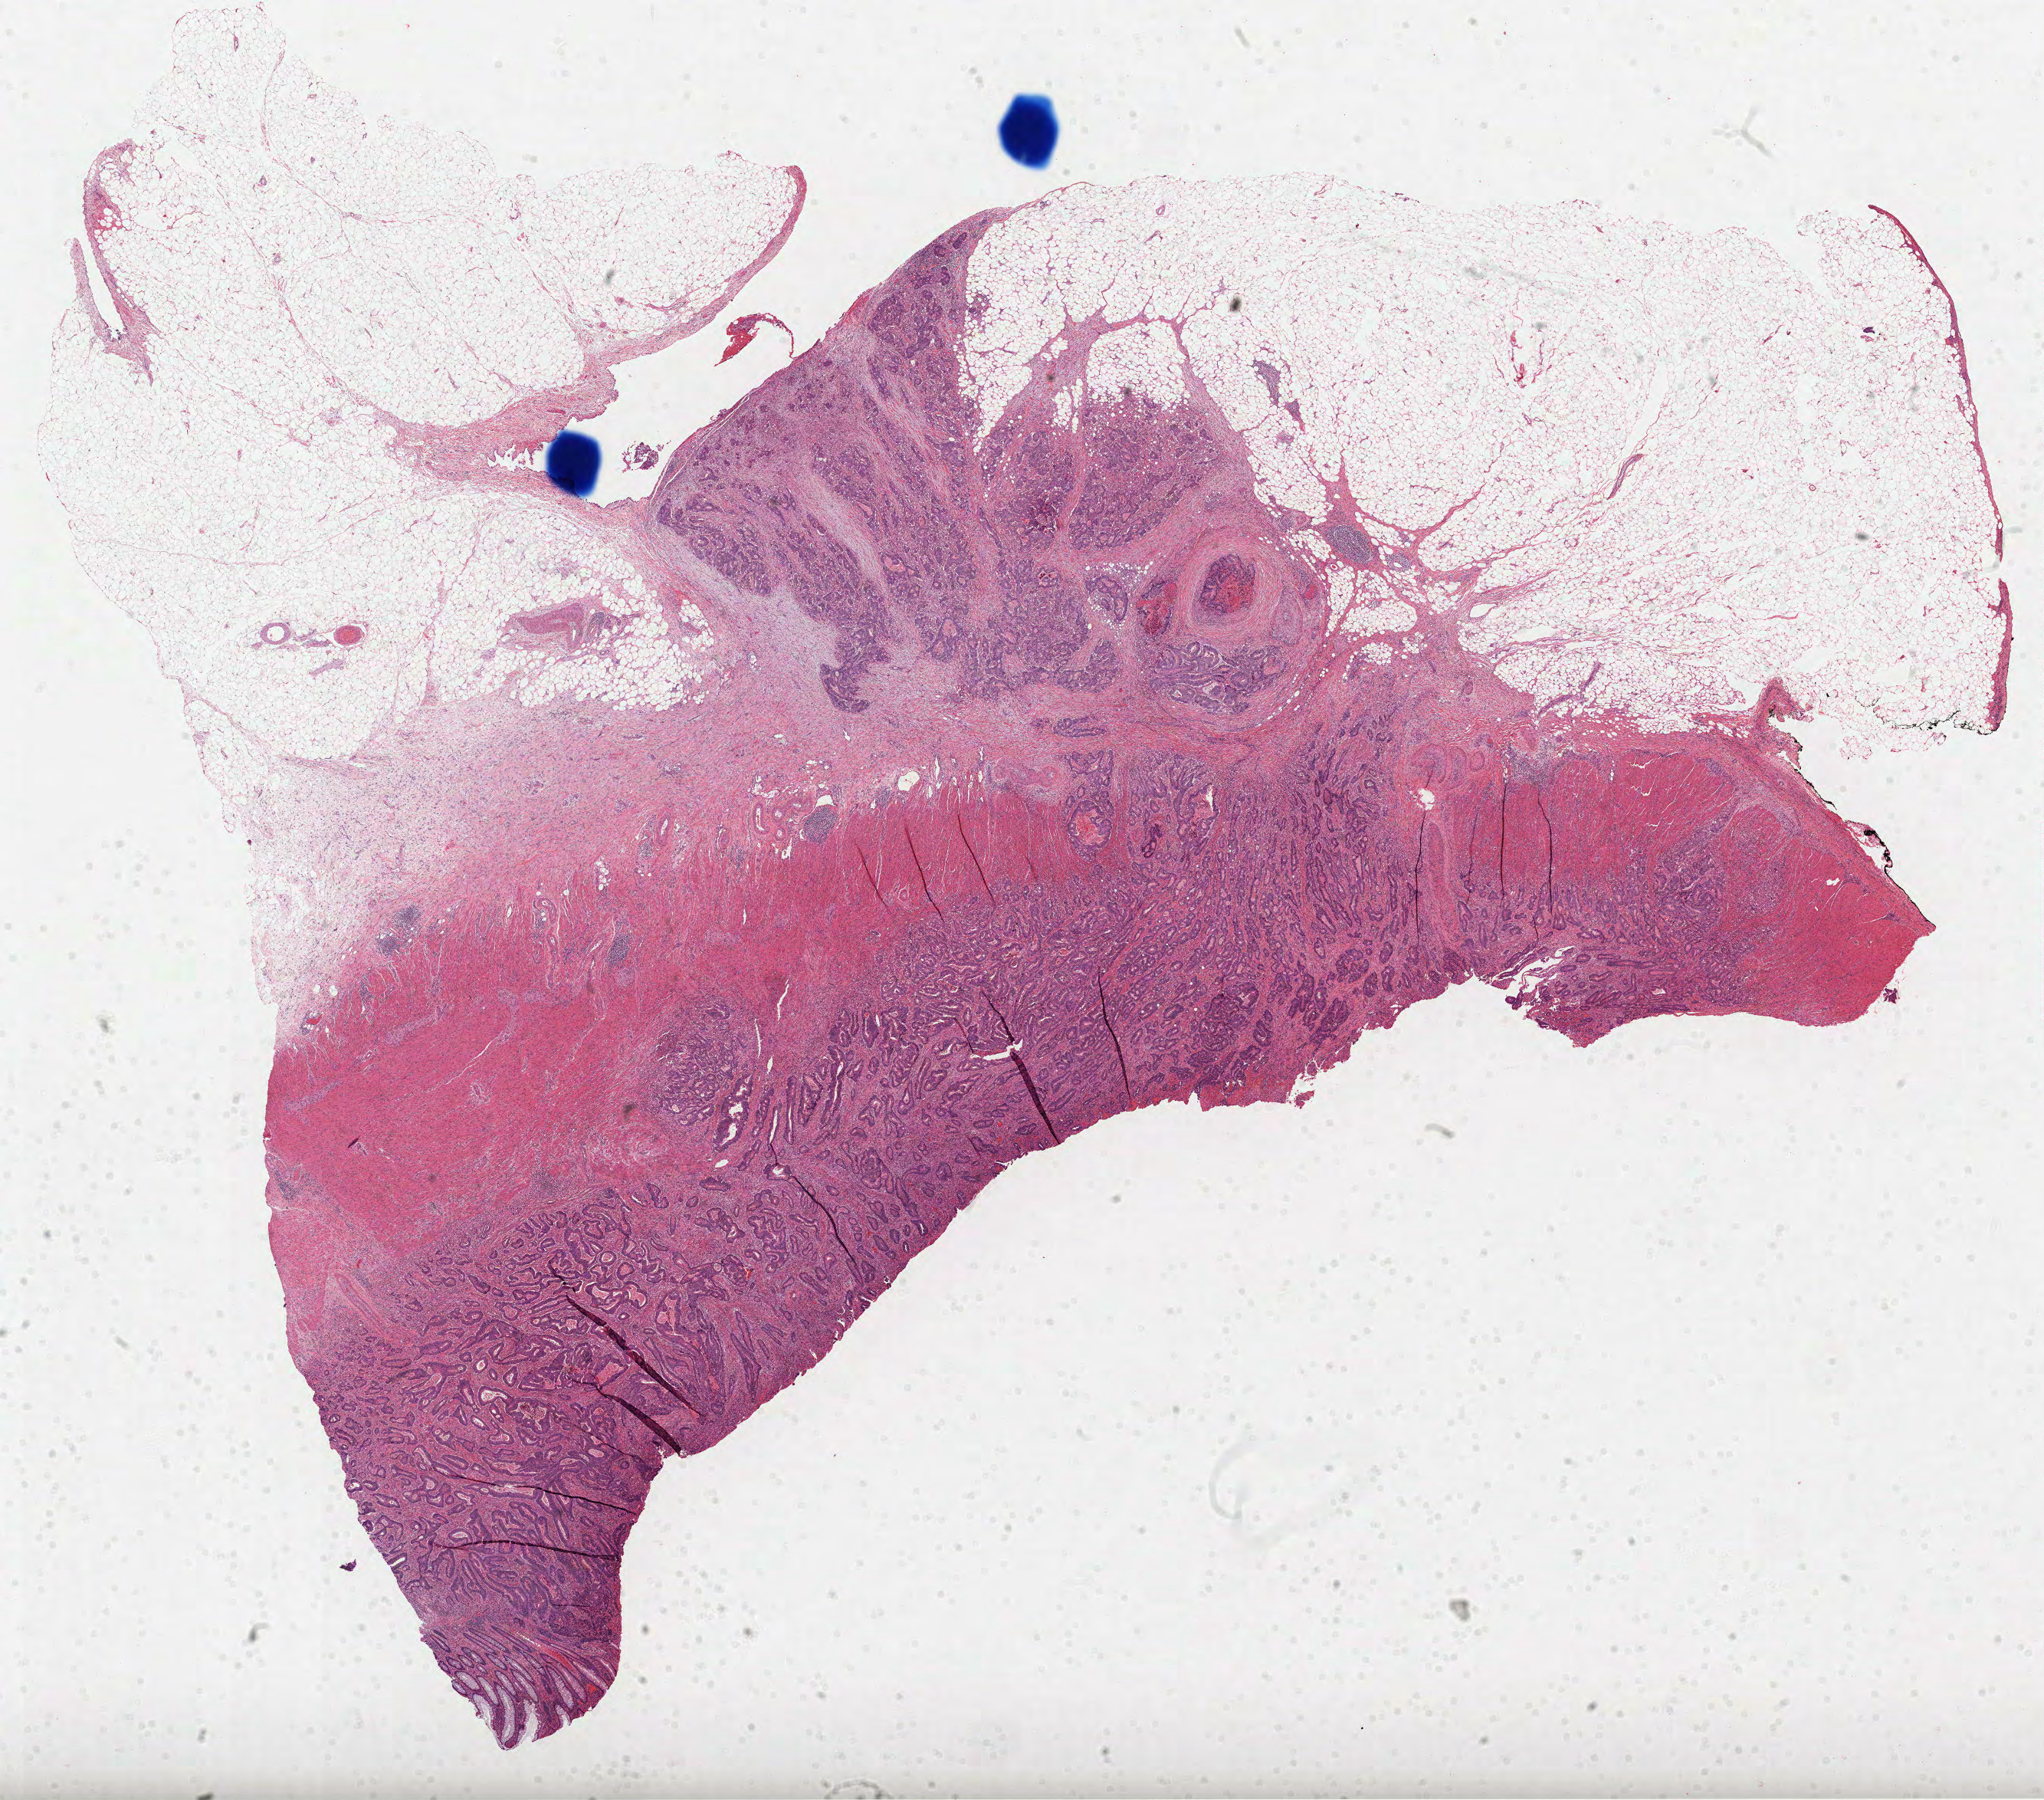
Whole-slide histology image, H&E, whole scanned area (about 21.5 x 18.9 mm) shown as a low-resolution overview, formalin-fixed paraffin-embedded (FFPE) diagnostic section, primary tumour sample from the colon. Female patient; age at initial diagnosis 47 years.
• diagnosis: Adenocarcinoma, NOS (sigmoid colon)
• AJCC pathologic stage: IIIB (6th edition)
• lymph nodes positive (case pathology): 3 of 14 examined